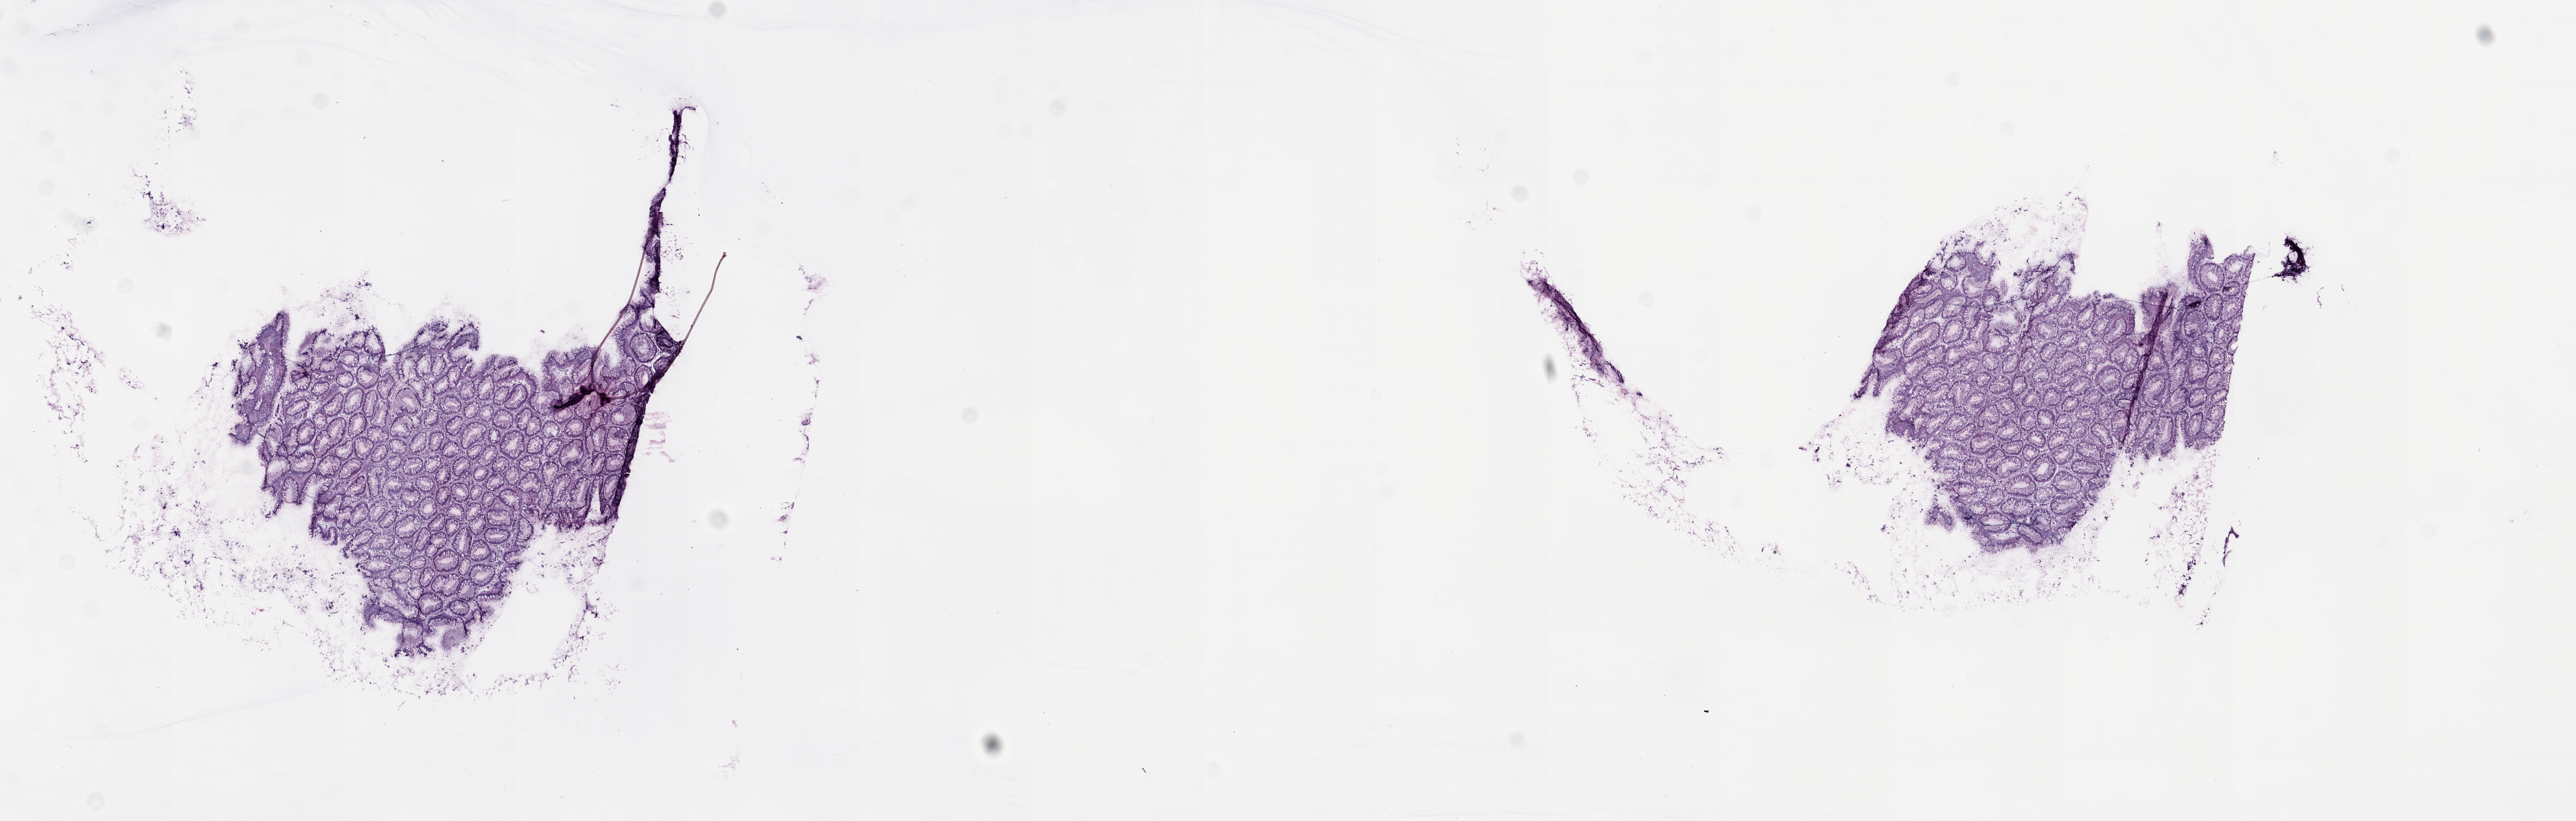
Digitized H&E-stained tissue section (whole slide), shown as a low-resolution overview of the whole scanned area (about 14.9 x 4.7 mm). Frozen section from the top of the tissue portion. Solid tissue normal (non-tumour tissue) sample from the esophagus. Male, age 79 years at initial diagnosis. Composition of this section per pathologist review: tumour cells 0%, tumour nuclei 0%, normal cells 100%, stromal cells 0%, necrosis 0%. Infiltration values recorded for this section: lymphocyte infiltration 1%, monocyte infiltration 1%, neutrophil infiltration 0%.
• this section: solid tissue normal (non-tumour) sample from the same patient
• patient diagnosis: Adenocarcinoma, NOS (lower third of esophagus)